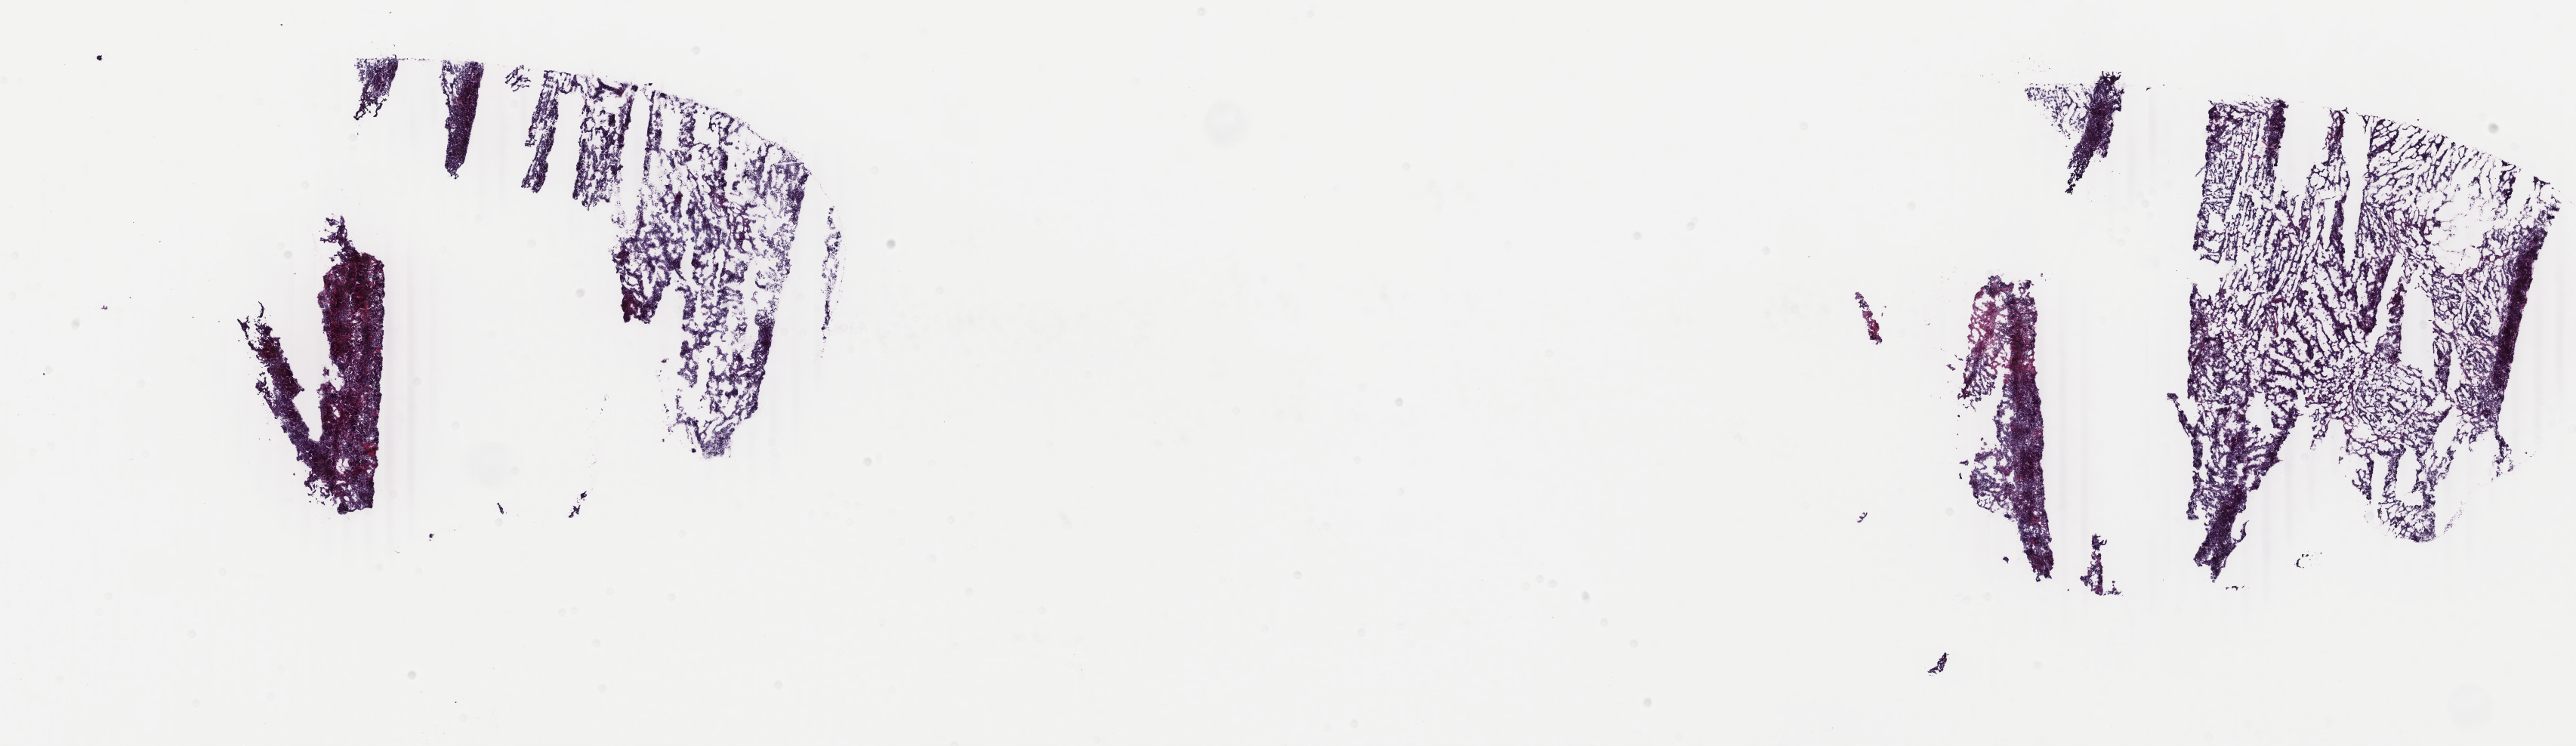
Digitized H&E-stained tissue section (whole slide), shown as a low-resolution overview of the whole scanned area (about 27.1 x 7.9 mm); frozen section from the top of the tissue portion; uterus, primary tumour sample. Patient: female, age at initial diagnosis 64 years.
Pathologic diagnosis: Endometrioid adenocarcinoma, NOS (endometrium).